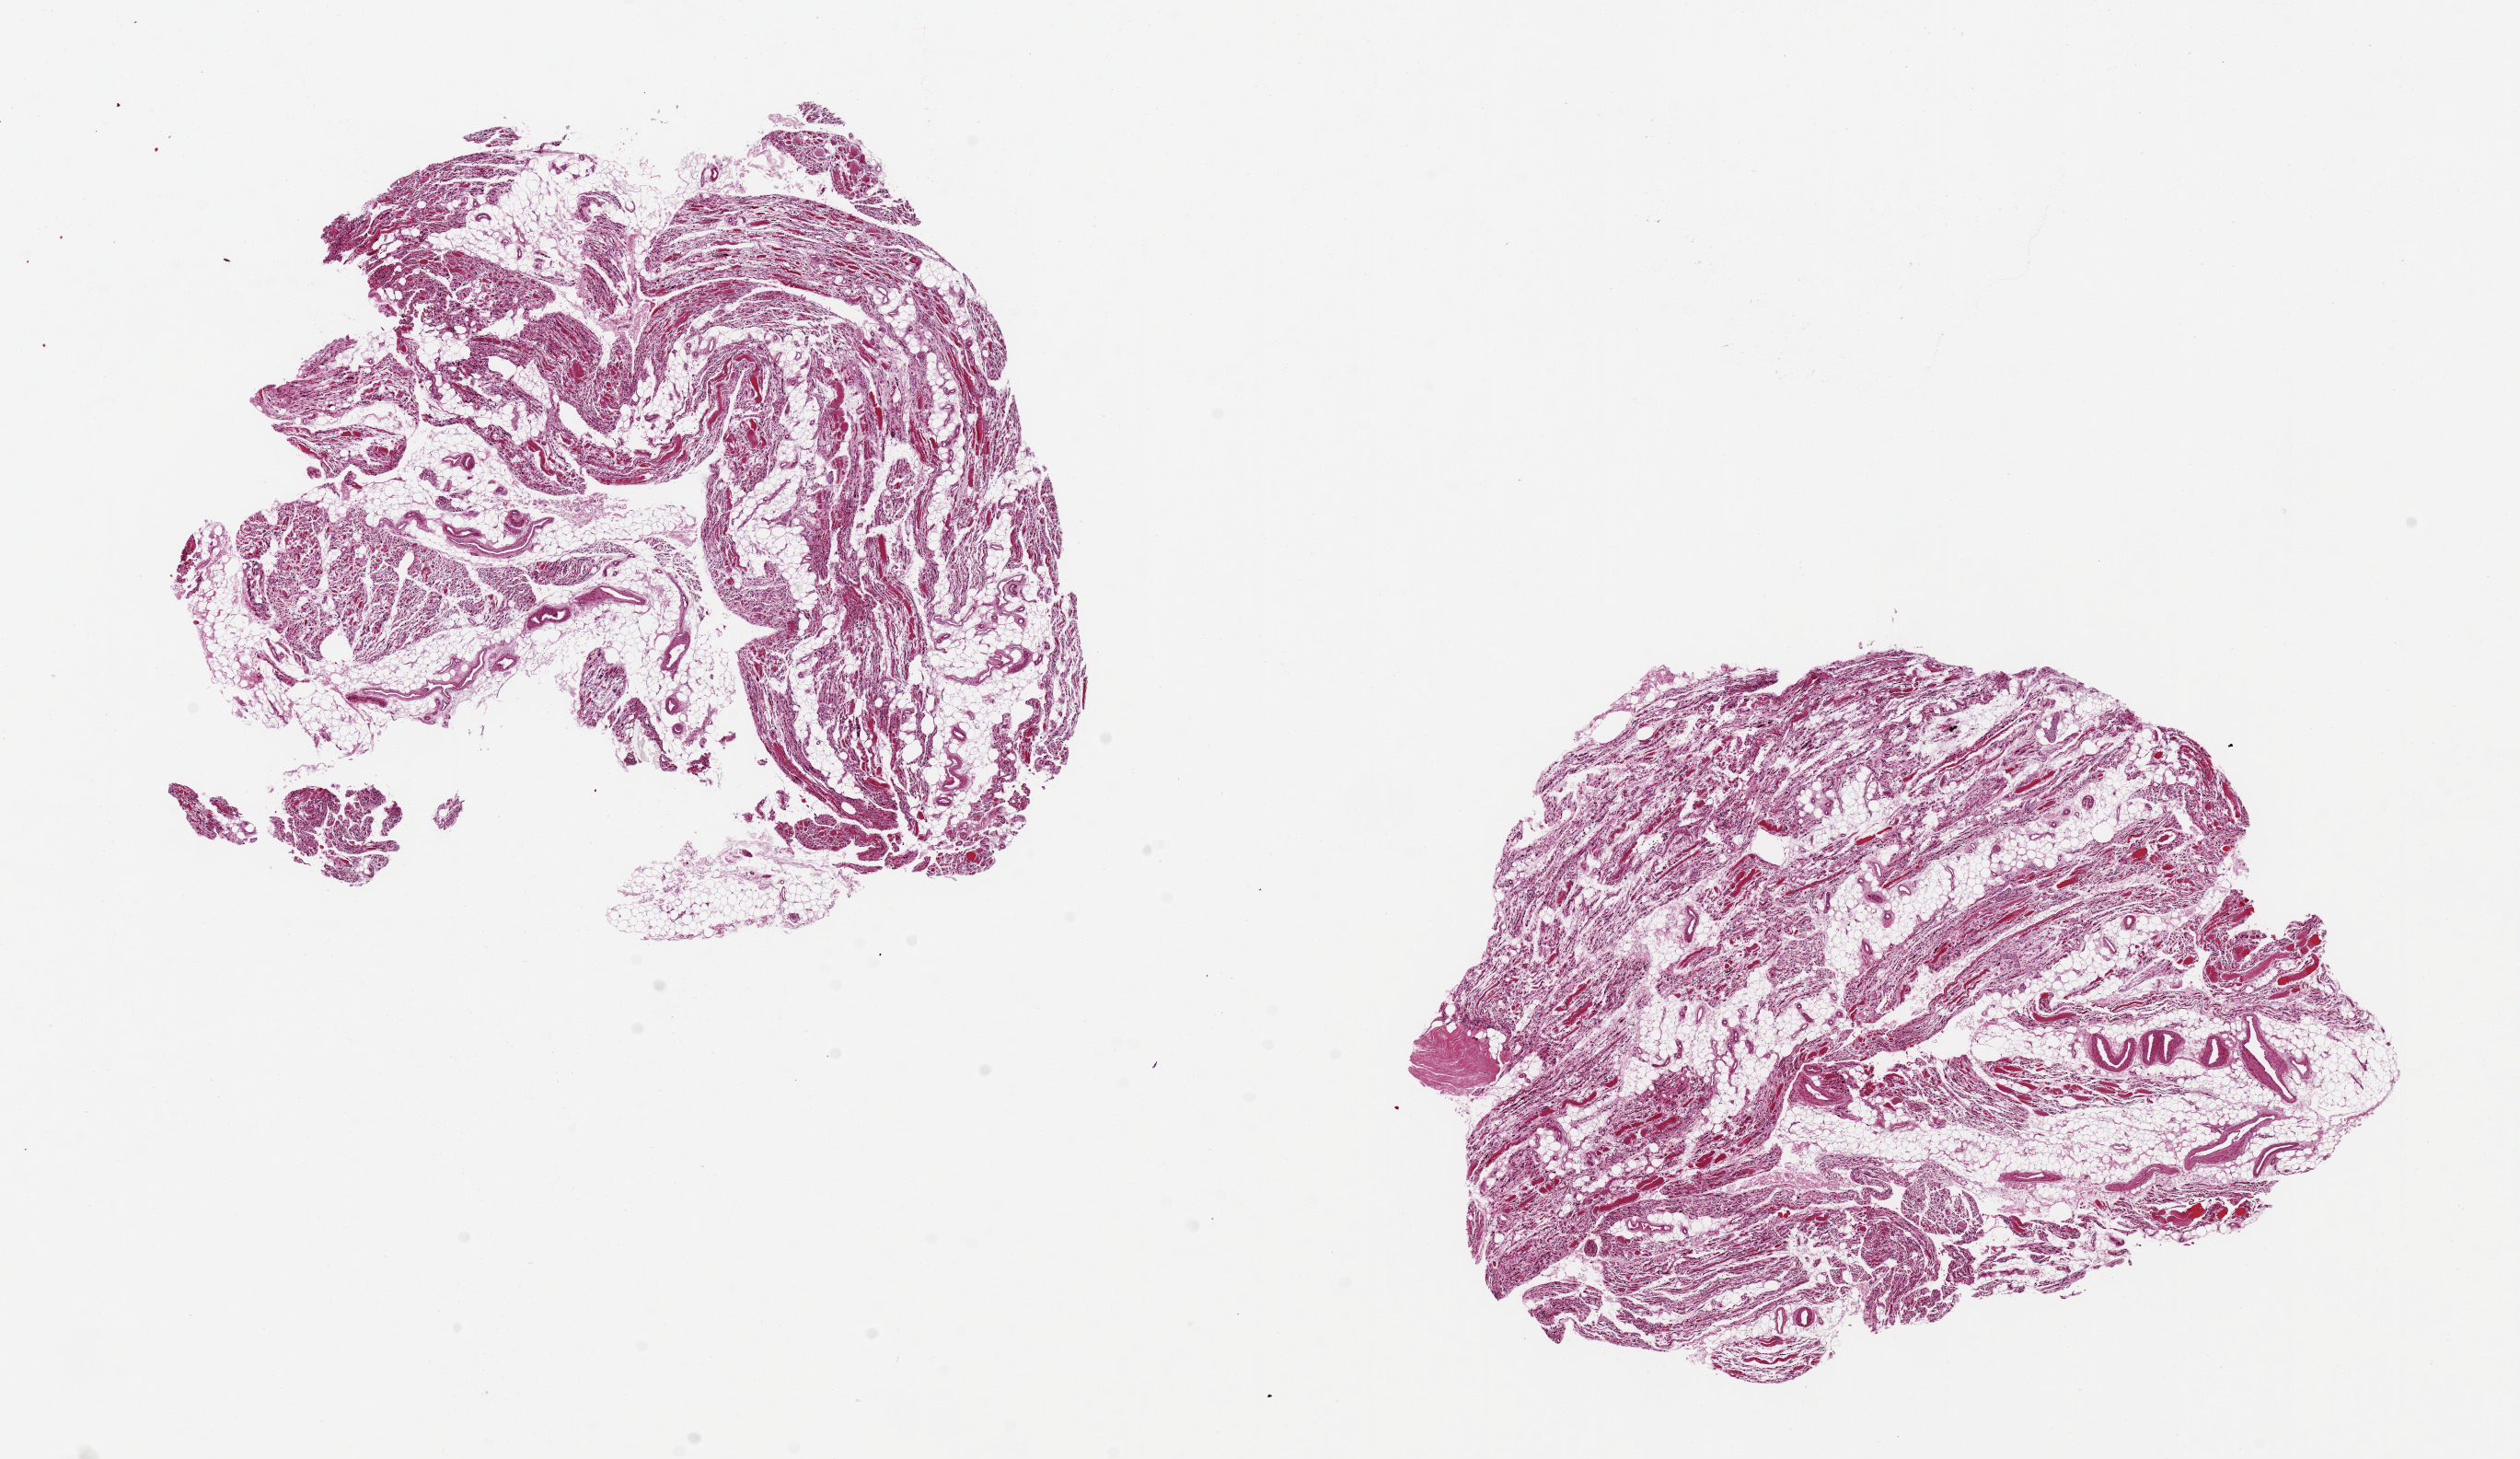
Digitized hematoxylin and eosin (H&E)-stained section, a low-resolution overview of the entire scanned area, about 21.7 x 12.5 mm (slide scanned at 20x). PAXgene-fixed, paraffin-embedded tissue. Section of skeletal muscle (target tissue). Donor tissue sample. Donor: male.
- pathologist's review note for this sample: 2 pieces, 8x7 & 8x6mm; severely atrophic with 20-30% internal adipose, probably due to ischemia